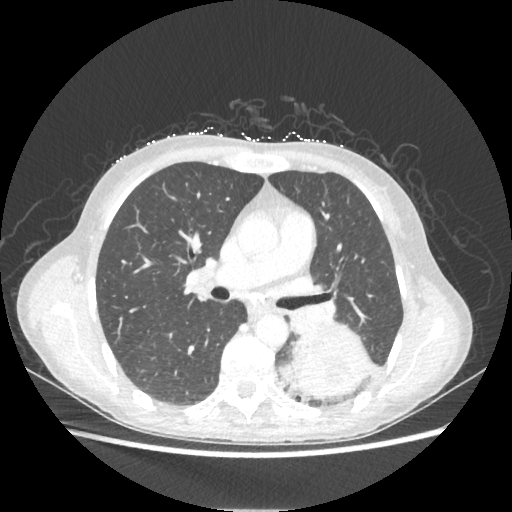
Chest CT, one axial slice; lung window (W 1500 / L -600 HU); 1.25 mm slice thickness; 512 × 512 image matrix, field of view 360 × 360 mm. Patient: female, 53 years. From the clinical record (not read from this slice): clinical TNM (as recorded): T3 N0 M0.
Structures marked on this image (bounding box drawn by a radiologist):
- lung tumour (recorded histology: adenocarcinoma): bounding box <287,328,372,397> (left, top, right, bottom; pixels)